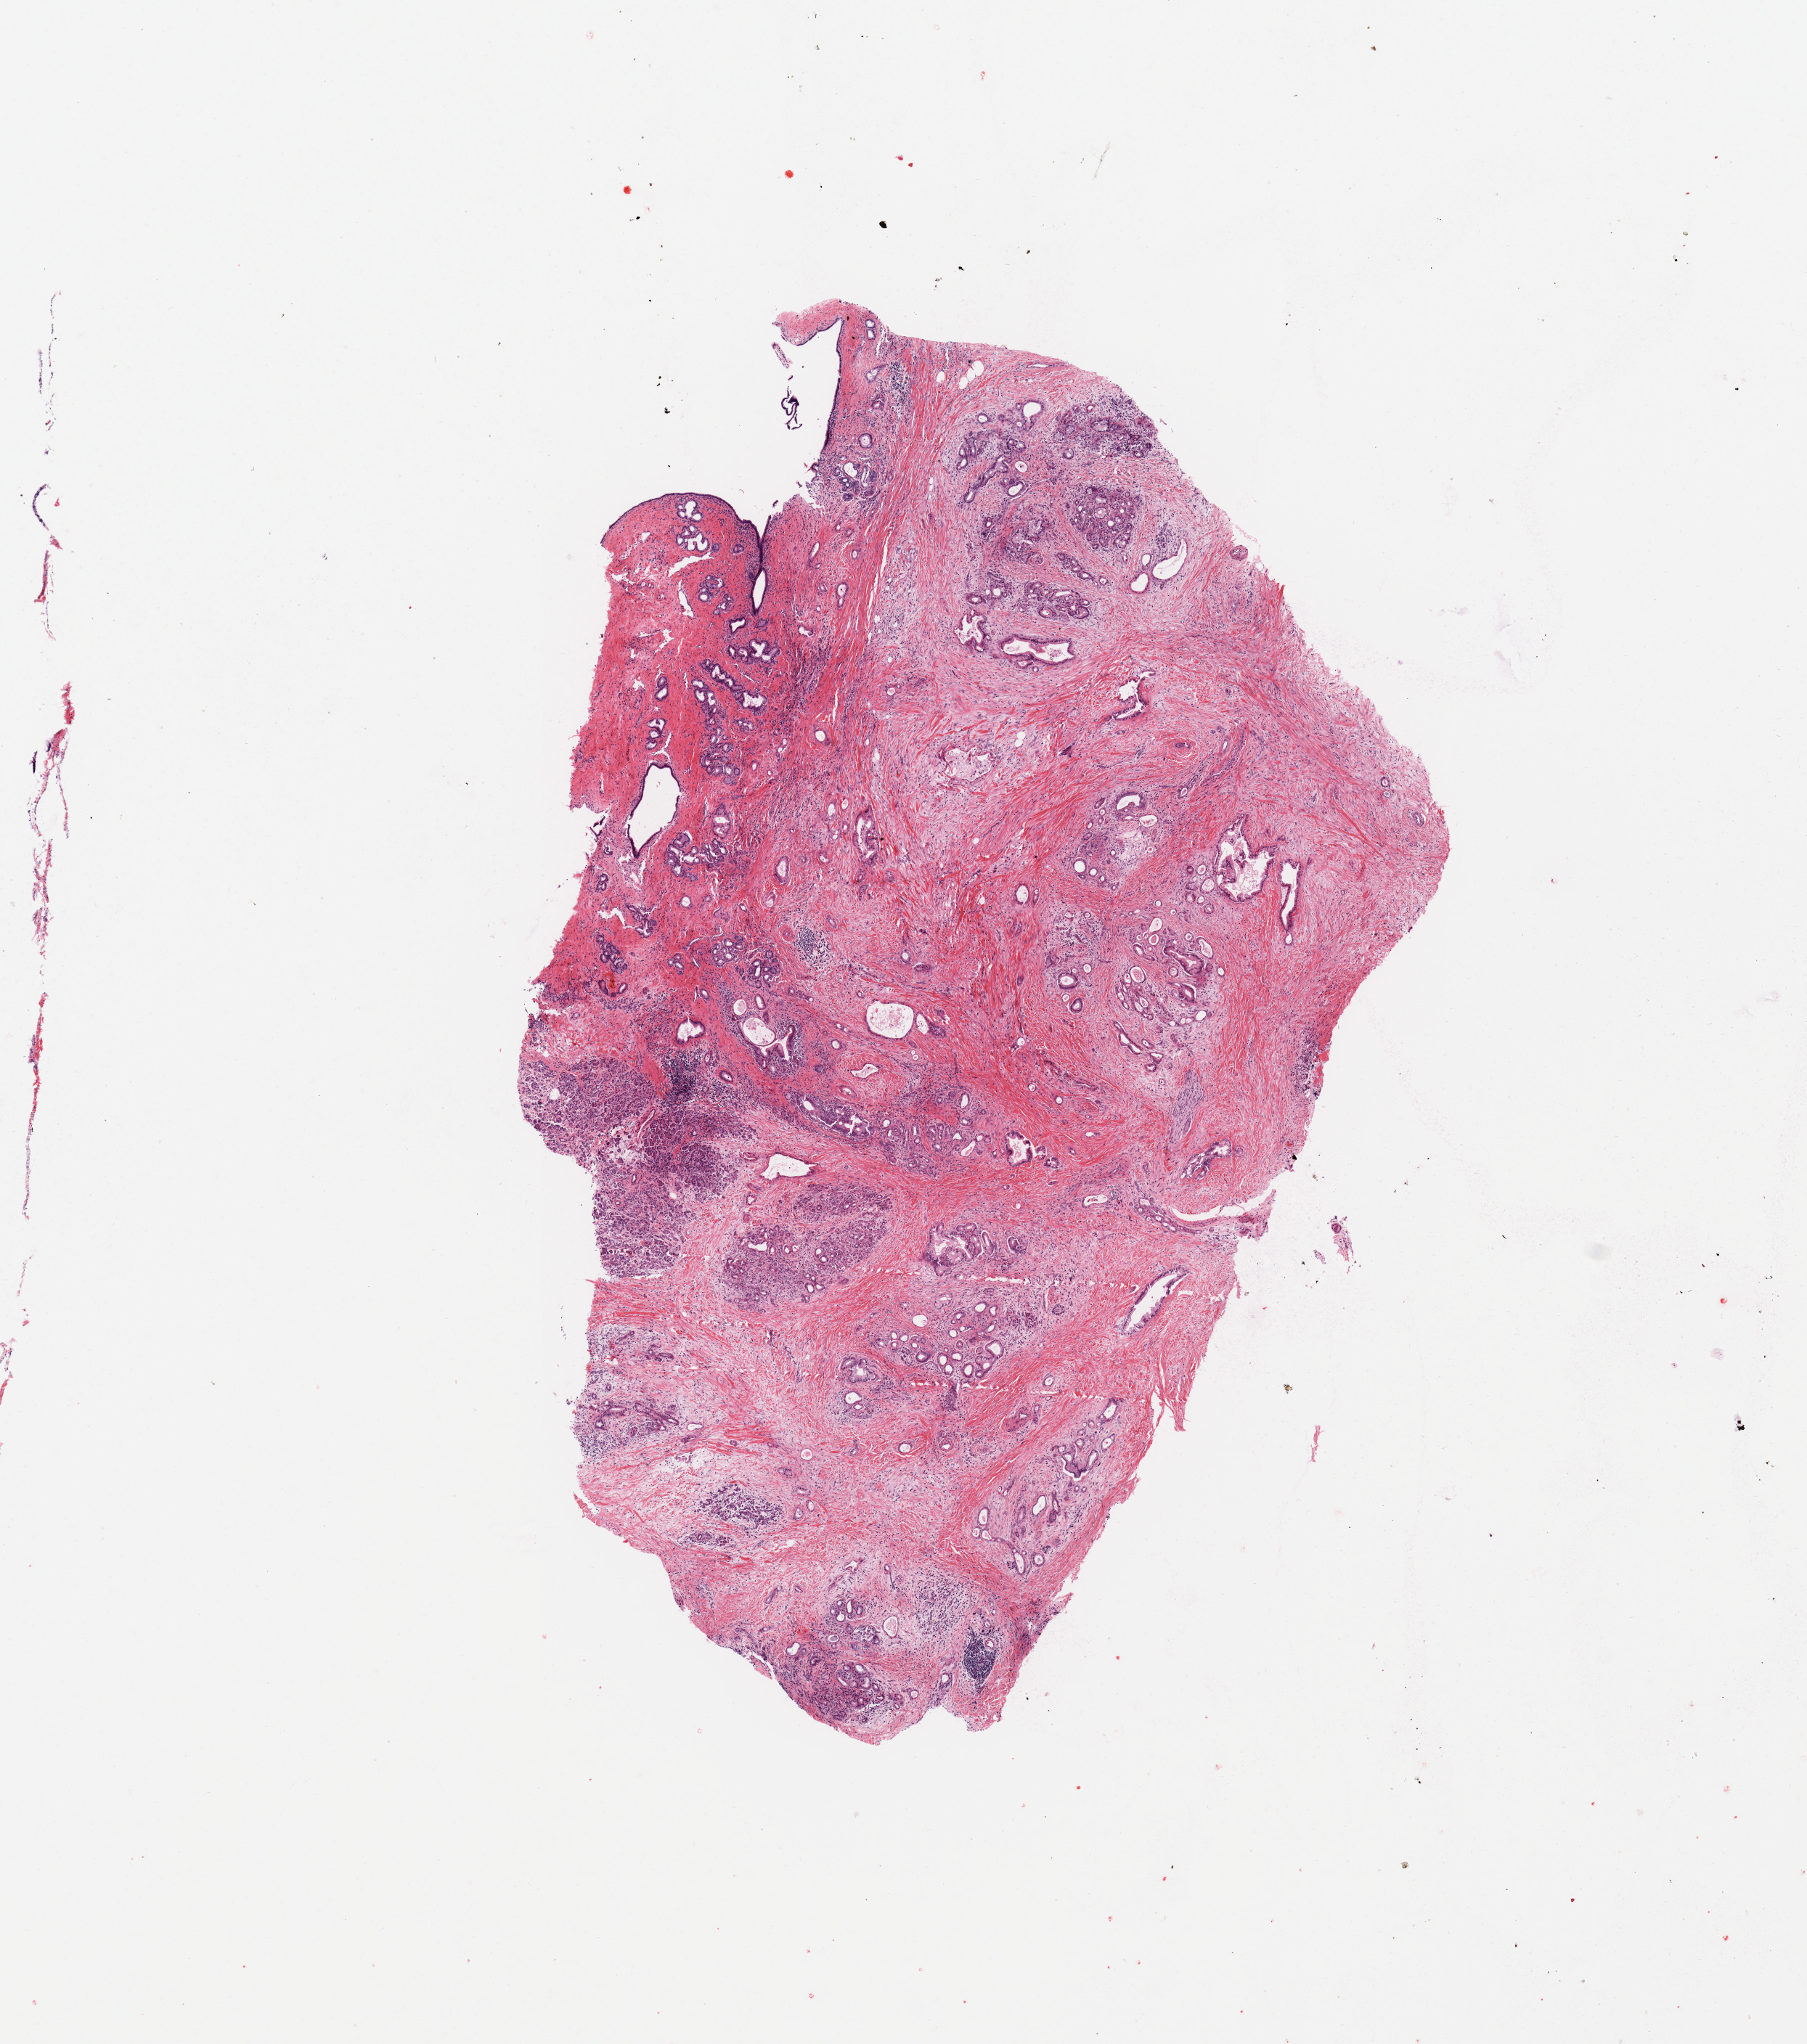
Whole-slide histology image, H&E-stained — whole scanned area (about 9.8 x 11.1 mm) shown as a low-resolution overview; tumour tissue sample, sampled site: pancreas. 43-year-old male patient. Histologic grade: G2 (moderately differentiated). Pathologist review of this section (percent, as recorded): tumour nuclei 20%, necrosis 0%.
AJCC pathologic stage: III. Primary tumour site (as recorded): head. Diagnosis: Infiltrating duct carcinoma, NOS.